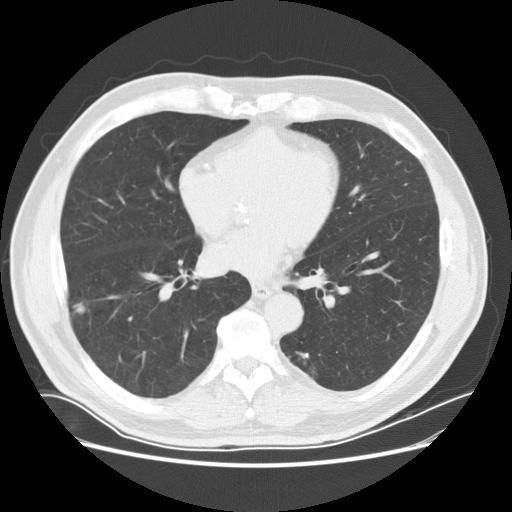
Axial slice from a low-dose chest CT screening exam; first (baseline) screen; lung window (W 1500 / L -600 HU); slice 92 of 170 in the series. Male participant, aged 72 years at enrolment. Current smoker at enrolment.
Expert-annotated lung lesion, bounding box <62,293,94,324> (left, top, right, bottom; pixels). The exam's reader record, not a measurement of the box and not confirmed to be the same lesion: non-calcified nodule or mass ≥4 mm, right lower lobe, 13 × 8 mm, poorly defined margins, soft tissue attenuation. Official screen result: positive, change unspecified: nodule(s) >= 4 mm or enlarging nodule(s), mass(es), or other non-specific abnormalities suspicious for lung cancer.